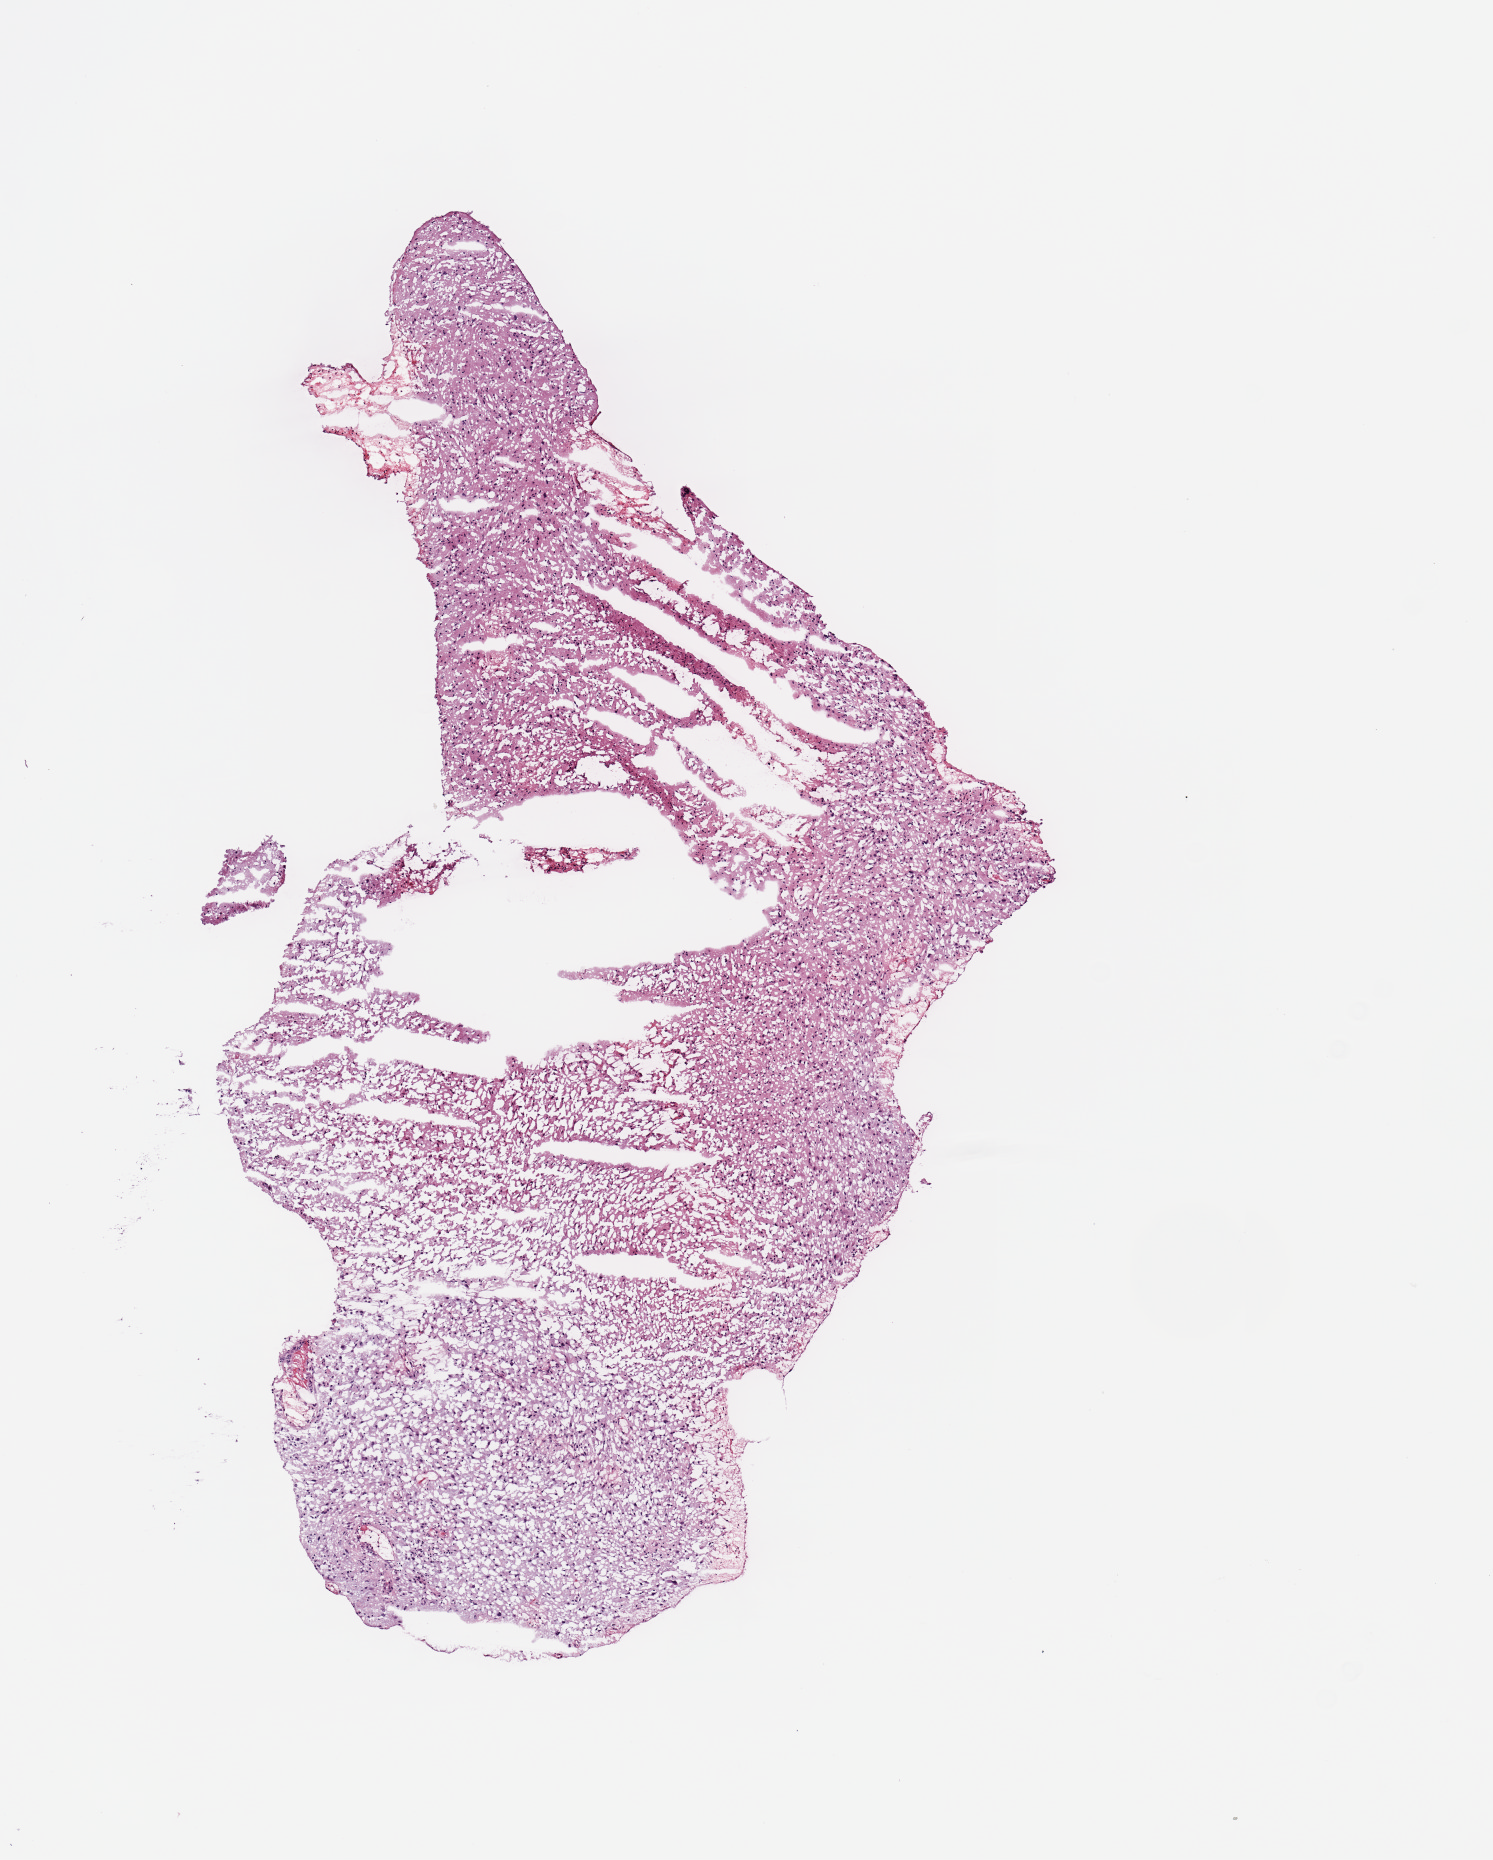
Digitized H&E tissue section (whole slide), a low-resolution overview of the entire scanned area, about 5.9 x 7.4 mm, brain, tumour tissue. Female, 57 y/o.
- primary tumour site (as recorded): temporal lobe
- patient diagnosis (cohort enrolment): glioblastoma multiforme (brain)